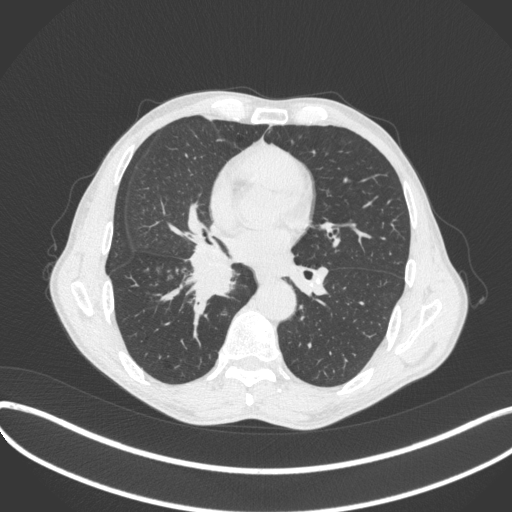
Chest CT, one axial slice. Slice 212 of 481 in the series (ordered by position). Lung window (W 1500 / L -600 HU). 512 × 512 image matrix, field of view 400 × 400 mm. Male patient, age 65 years. Case-level facts recorded for this patient, not image findings: clinical TNM (as recorded): T2a N0 M0; histopathological grade: G2.
Outlined on this slice (rectangle marked by the reading radiologist):
- lung tumour (recorded histology: squamous cell carcinoma): bounding box (x1, y1, x2, y2) in pixels: (182, 243, 238, 301)